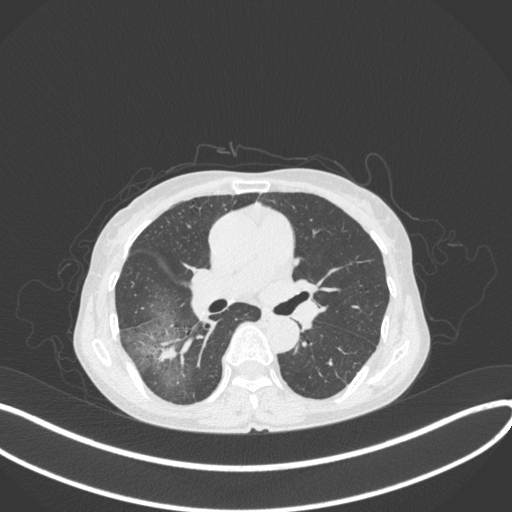
Chest CT, one axial slice. Position 223 of 379 along the scan axis. 120 kVp. Lung window (W 1500 / L -600 HU). 1 mm slice thickness. 512 × 512 image matrix, field of view 400 × 400 mm. Patient: female, 69 years. Case-level facts recorded for this patient, not image findings: clinical TNM (as recorded): T1b N0 M0; histopathological grade: G2-3.
Annotated regions visible in this slice (bounding box drawn by a radiologist):
- lung tumour (recorded histology: adenocarcinoma): bounding box (x1, y1, x2, y2) in pixels: (155, 338, 192, 366)